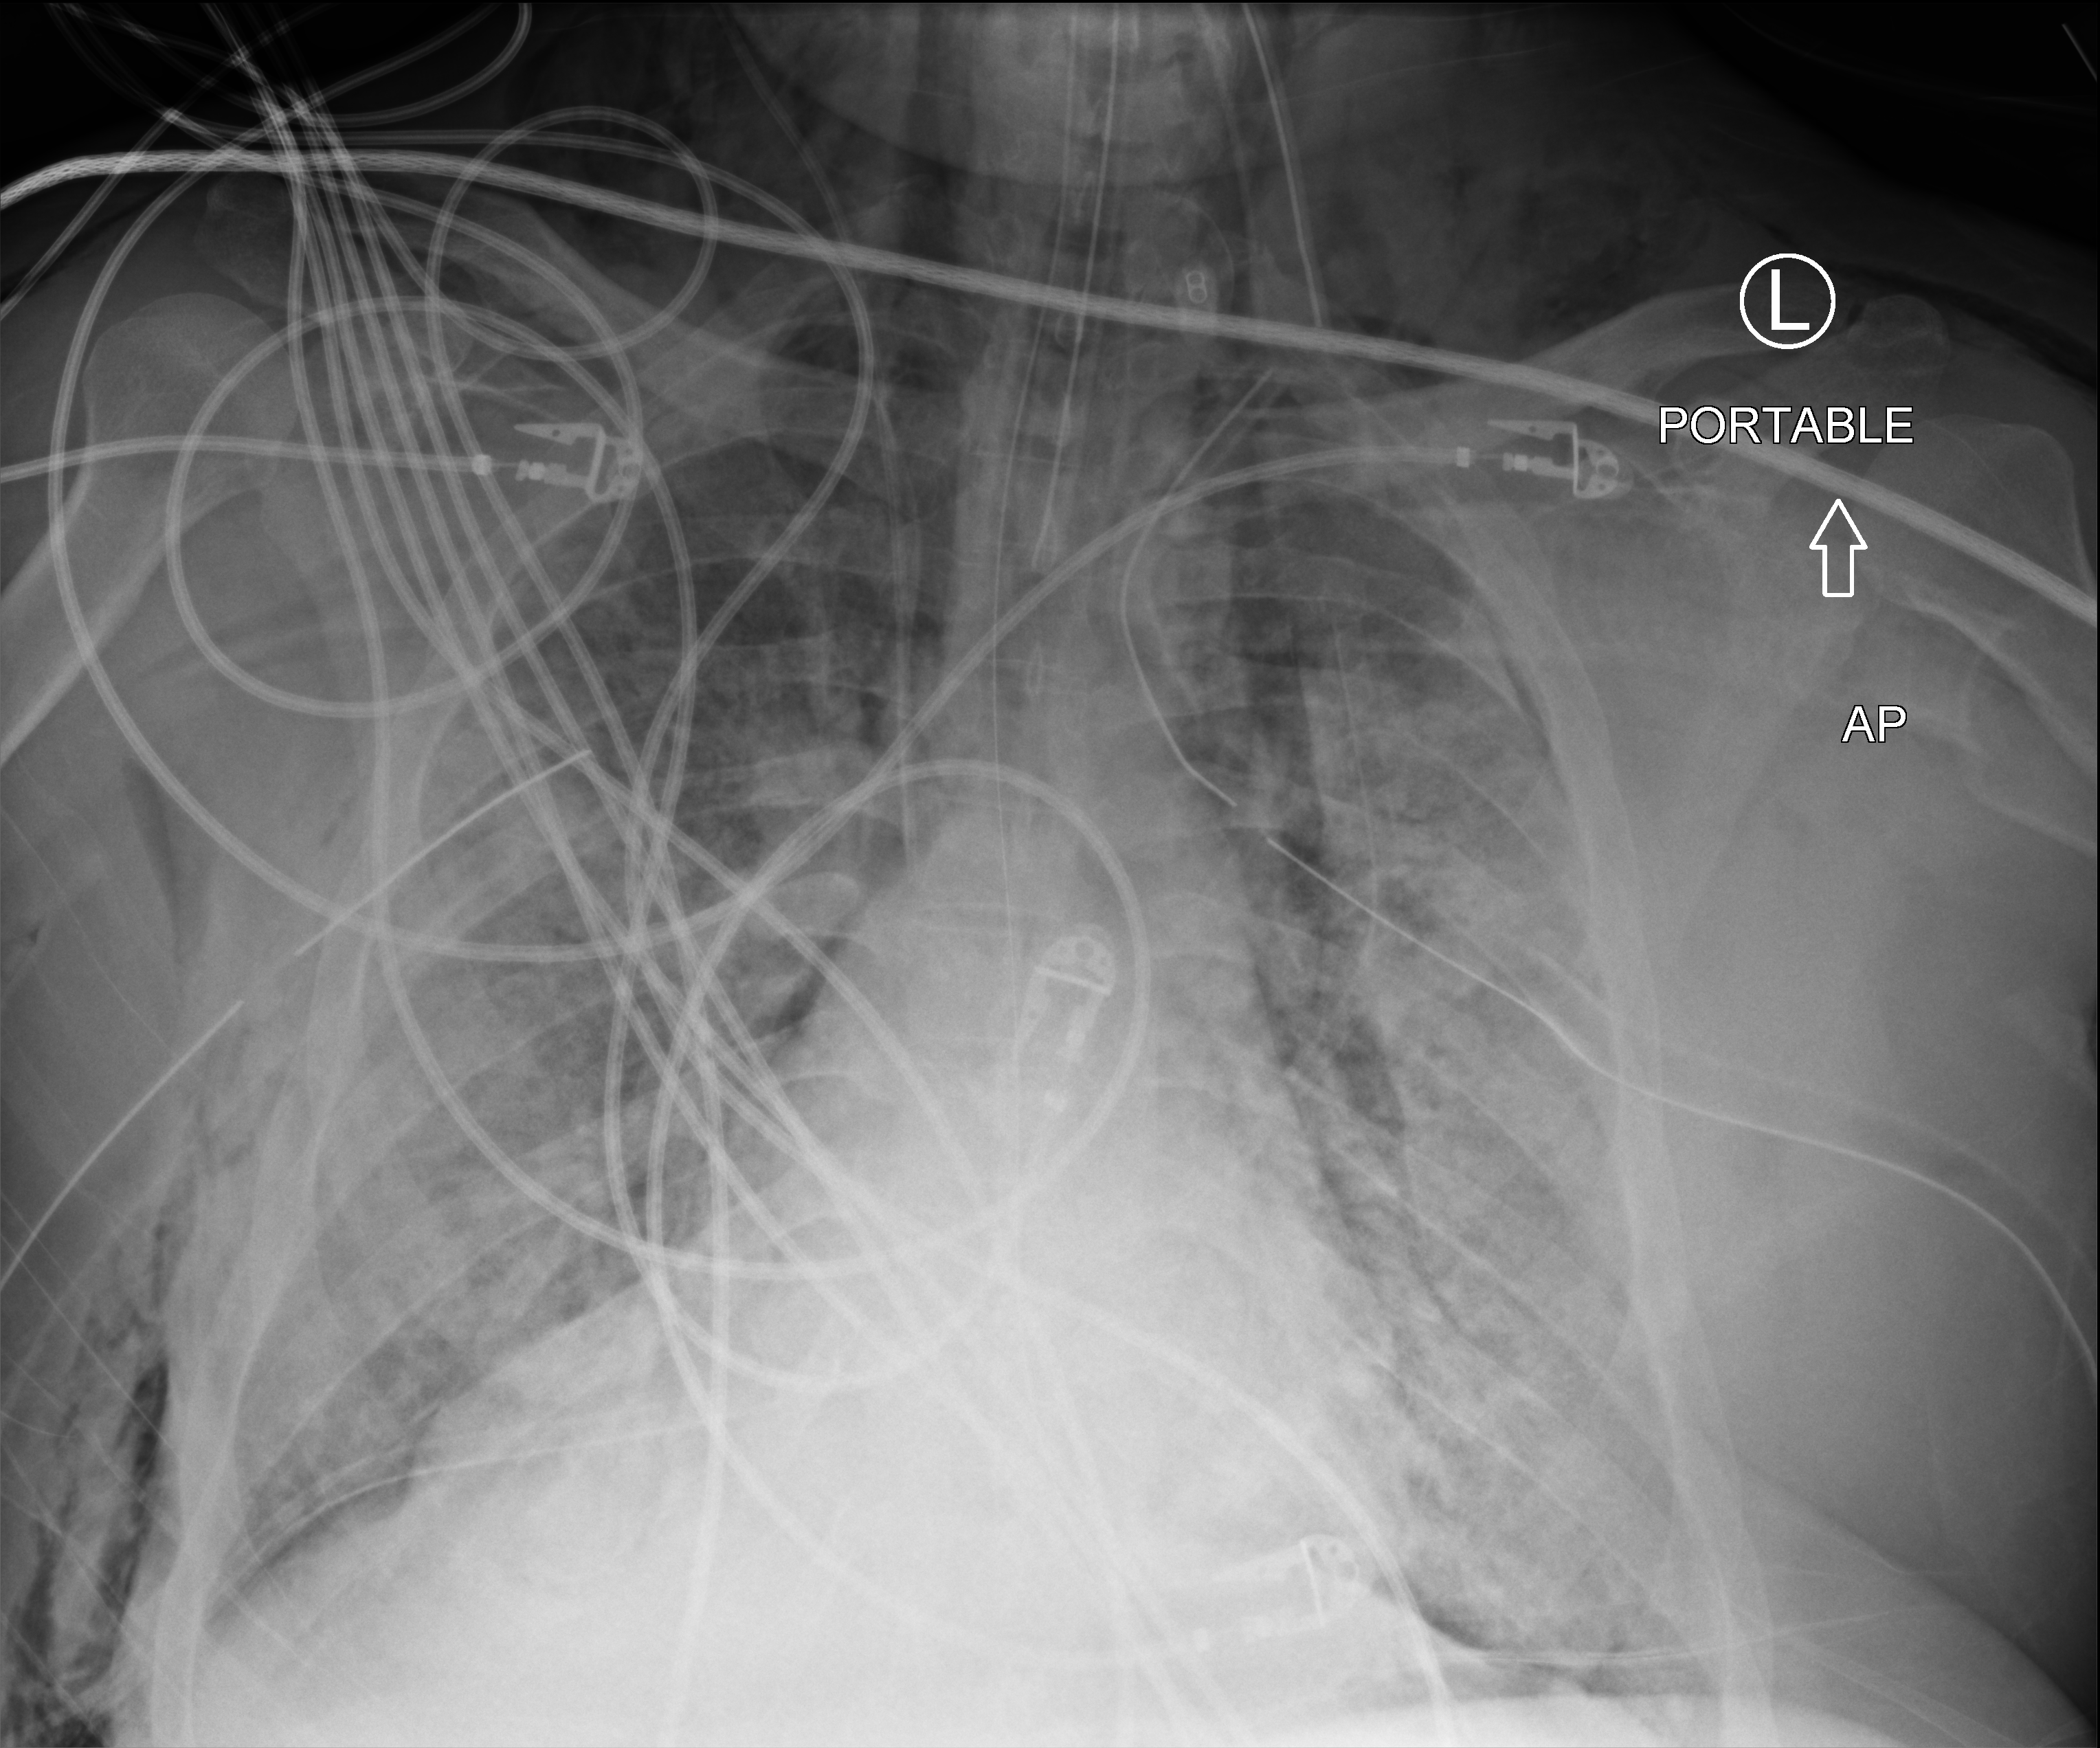
Bedside chest radiograph (computed radiography); anteroposterior (AP) projection. Patient hospitalised with COVID-19, aged 18–59 years.
From the hospital-stay record, not from the radiograph (when in the stay this image was taken is not recorded): admitted to intensive care during this hospital stay: yes; mechanically ventilated during this hospital stay: yes.